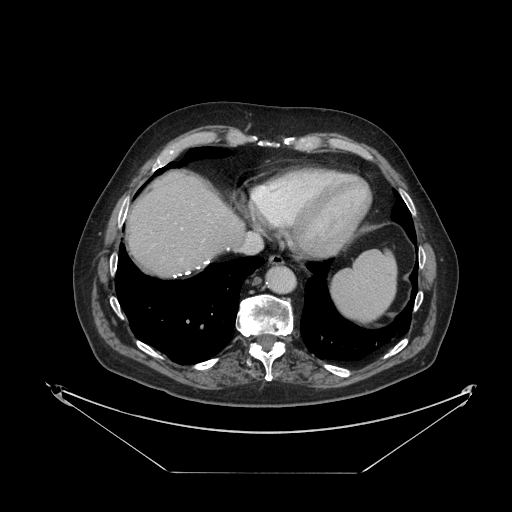
Contrast-enhanced abdominal CT, one axial slice; slice 107 of 121 in the series (ordered by position); reconstruction kernel STANDARD; 120 kVp; intravenous contrast given; soft-tissue window (W 400 / L 40 HU); 2.5 mm slice thickness; 512 × 512 image matrix, field of view 500 × 500 mm. Male patient, age 68 years. From the clinical record (not read from this slice): diagnosis: colorectal cancer liver metastases, imaged before liver resection; multiple liver metastases: no; largest metastasis: 4 cm; disease in both lobes: no.
Annotated regions visible in this slice (expert manual segmentation):
- liver: bounding box (x1, y1, x2, y2) in pixels: (129, 173, 244, 276)
- planned liver remnant (the part of the liver to remain after resection): (129, 174, 244, 276)